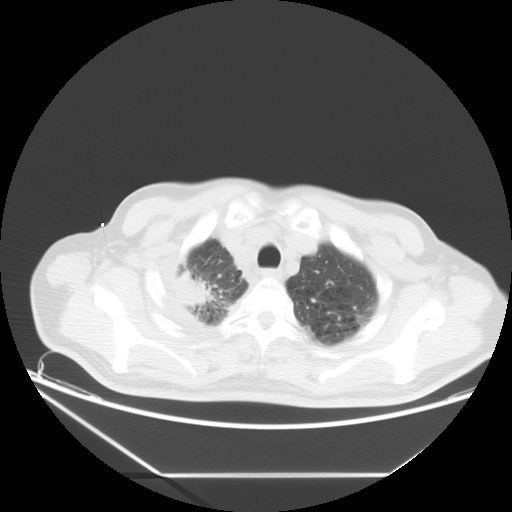
Chest CT, one axial slice; reconstruction kernel STANDARD; lung window (W 1500 / L -600 HU); 512 × 512 image matrix. Patient: male, 75 years. From the clinical record (not read from this slice): clinical TNM (as recorded): T1c N1 M1.
Structures marked on this image (rectangle marked by the reading radiologist):
- lung tumour (recorded histology: adenocarcinoma): box from (x=173, y=271) to (x=210, y=313) px